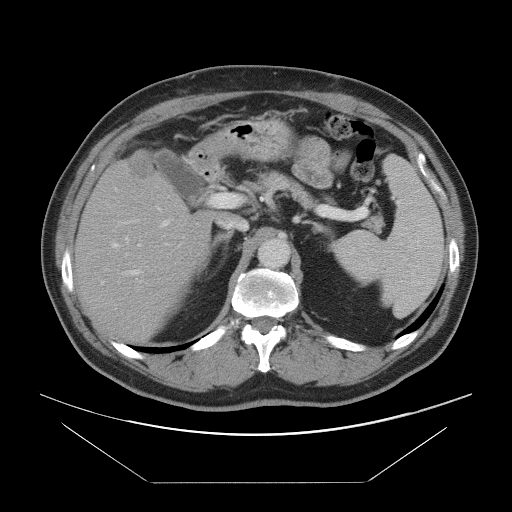
Contrast-enhanced abdominal CT, one axial slice. Intravenous contrast given. Soft-tissue window (W 400 / L 40 HU). 5 mm slice thickness. 512 × 512 image matrix. Male patient, age 62 years. From the clinical record (not read from this slice): diagnosis: colorectal cancer liver metastases, imaged before liver resection; multiple liver metastases: no; largest metastasis: 7 cm; disease in both lobes: yes.
Structures marked on this image (manually delineated by an expert):
- hepatic veins: bounding box (x1, y1, x2, y2) in pixels: (112, 186, 169, 256)
- liver: (76, 154, 213, 343)
- planned liver remnant (the part of the liver to remain after resection): (76, 176, 212, 343)
- portal vein (with intrahepatic branches): (123, 193, 228, 272)
- liver metastasis: (129, 157, 155, 180)